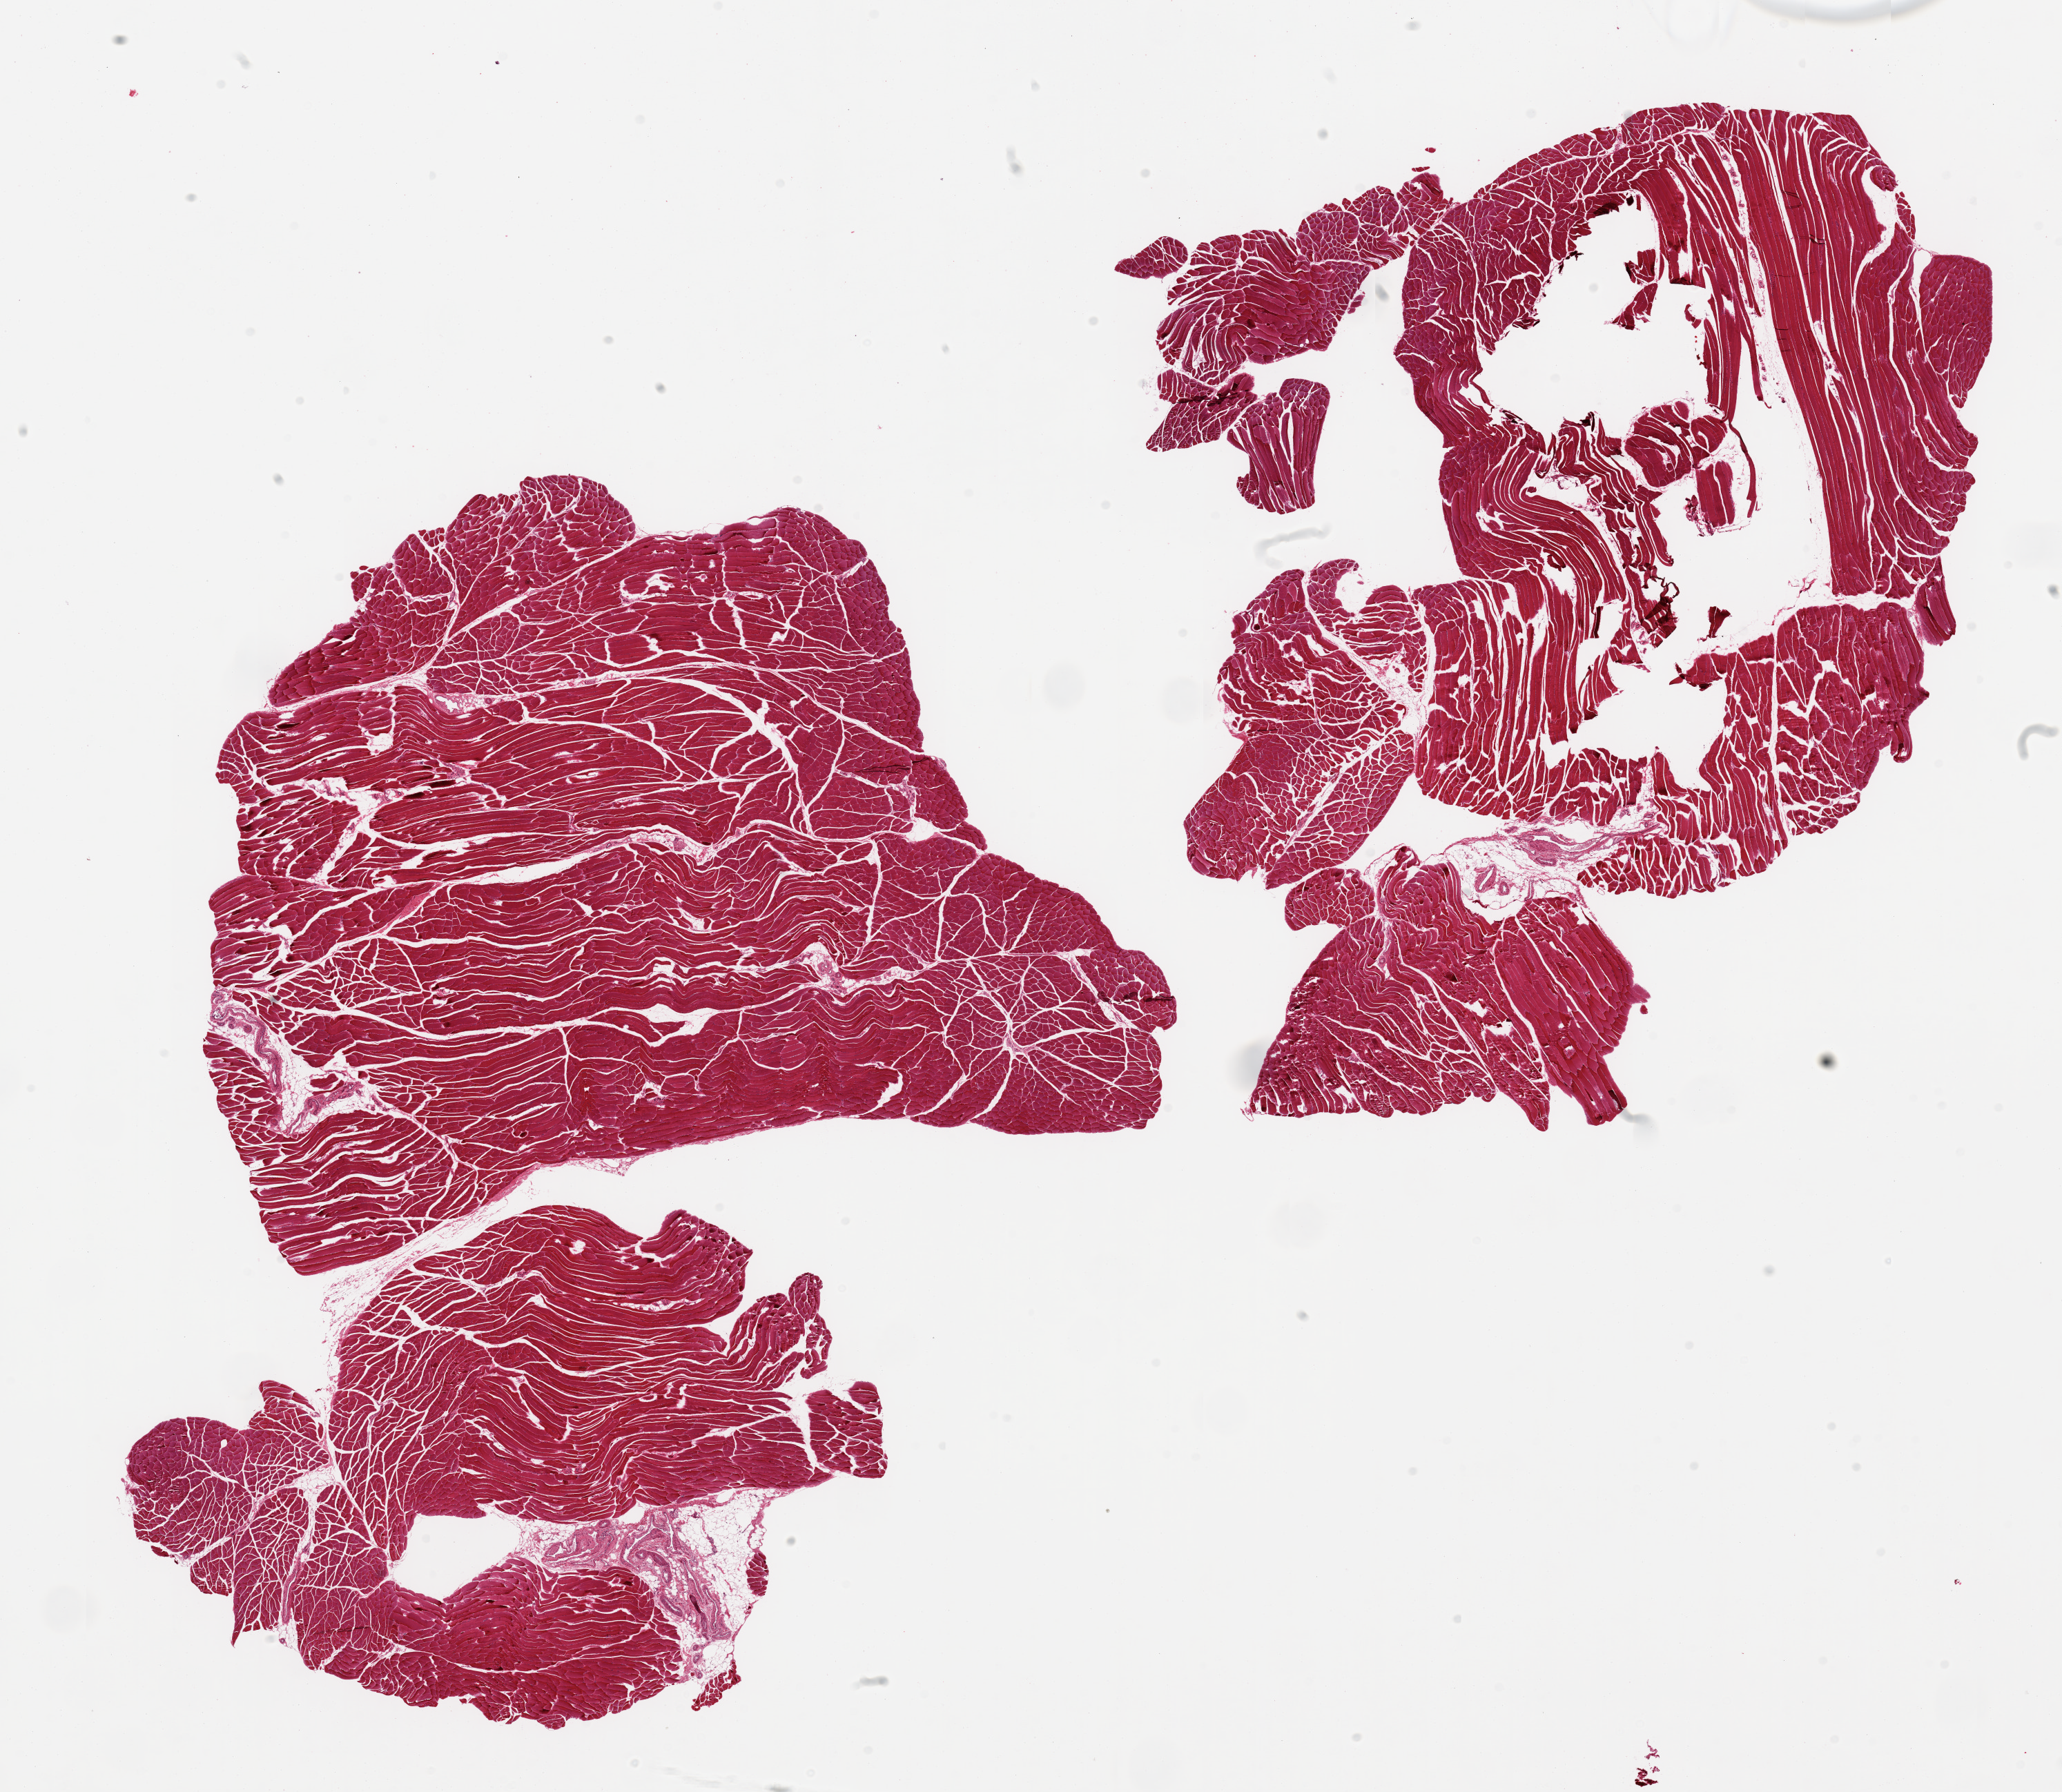
Digitized hematoxylin and eosin (H&E)-stained section — low-resolution overview of the scanned area, about 23.6 x 20.5 mm (from a 20x scan). PAXgene-fixed paraffin-embedded (PFPE) section. Section of skeletal muscle (target tissue). Donor tissue sample.
- review note (as recorded): 2 pieces; central defect in 1 piece, otherwise includes minimal fat/vessels